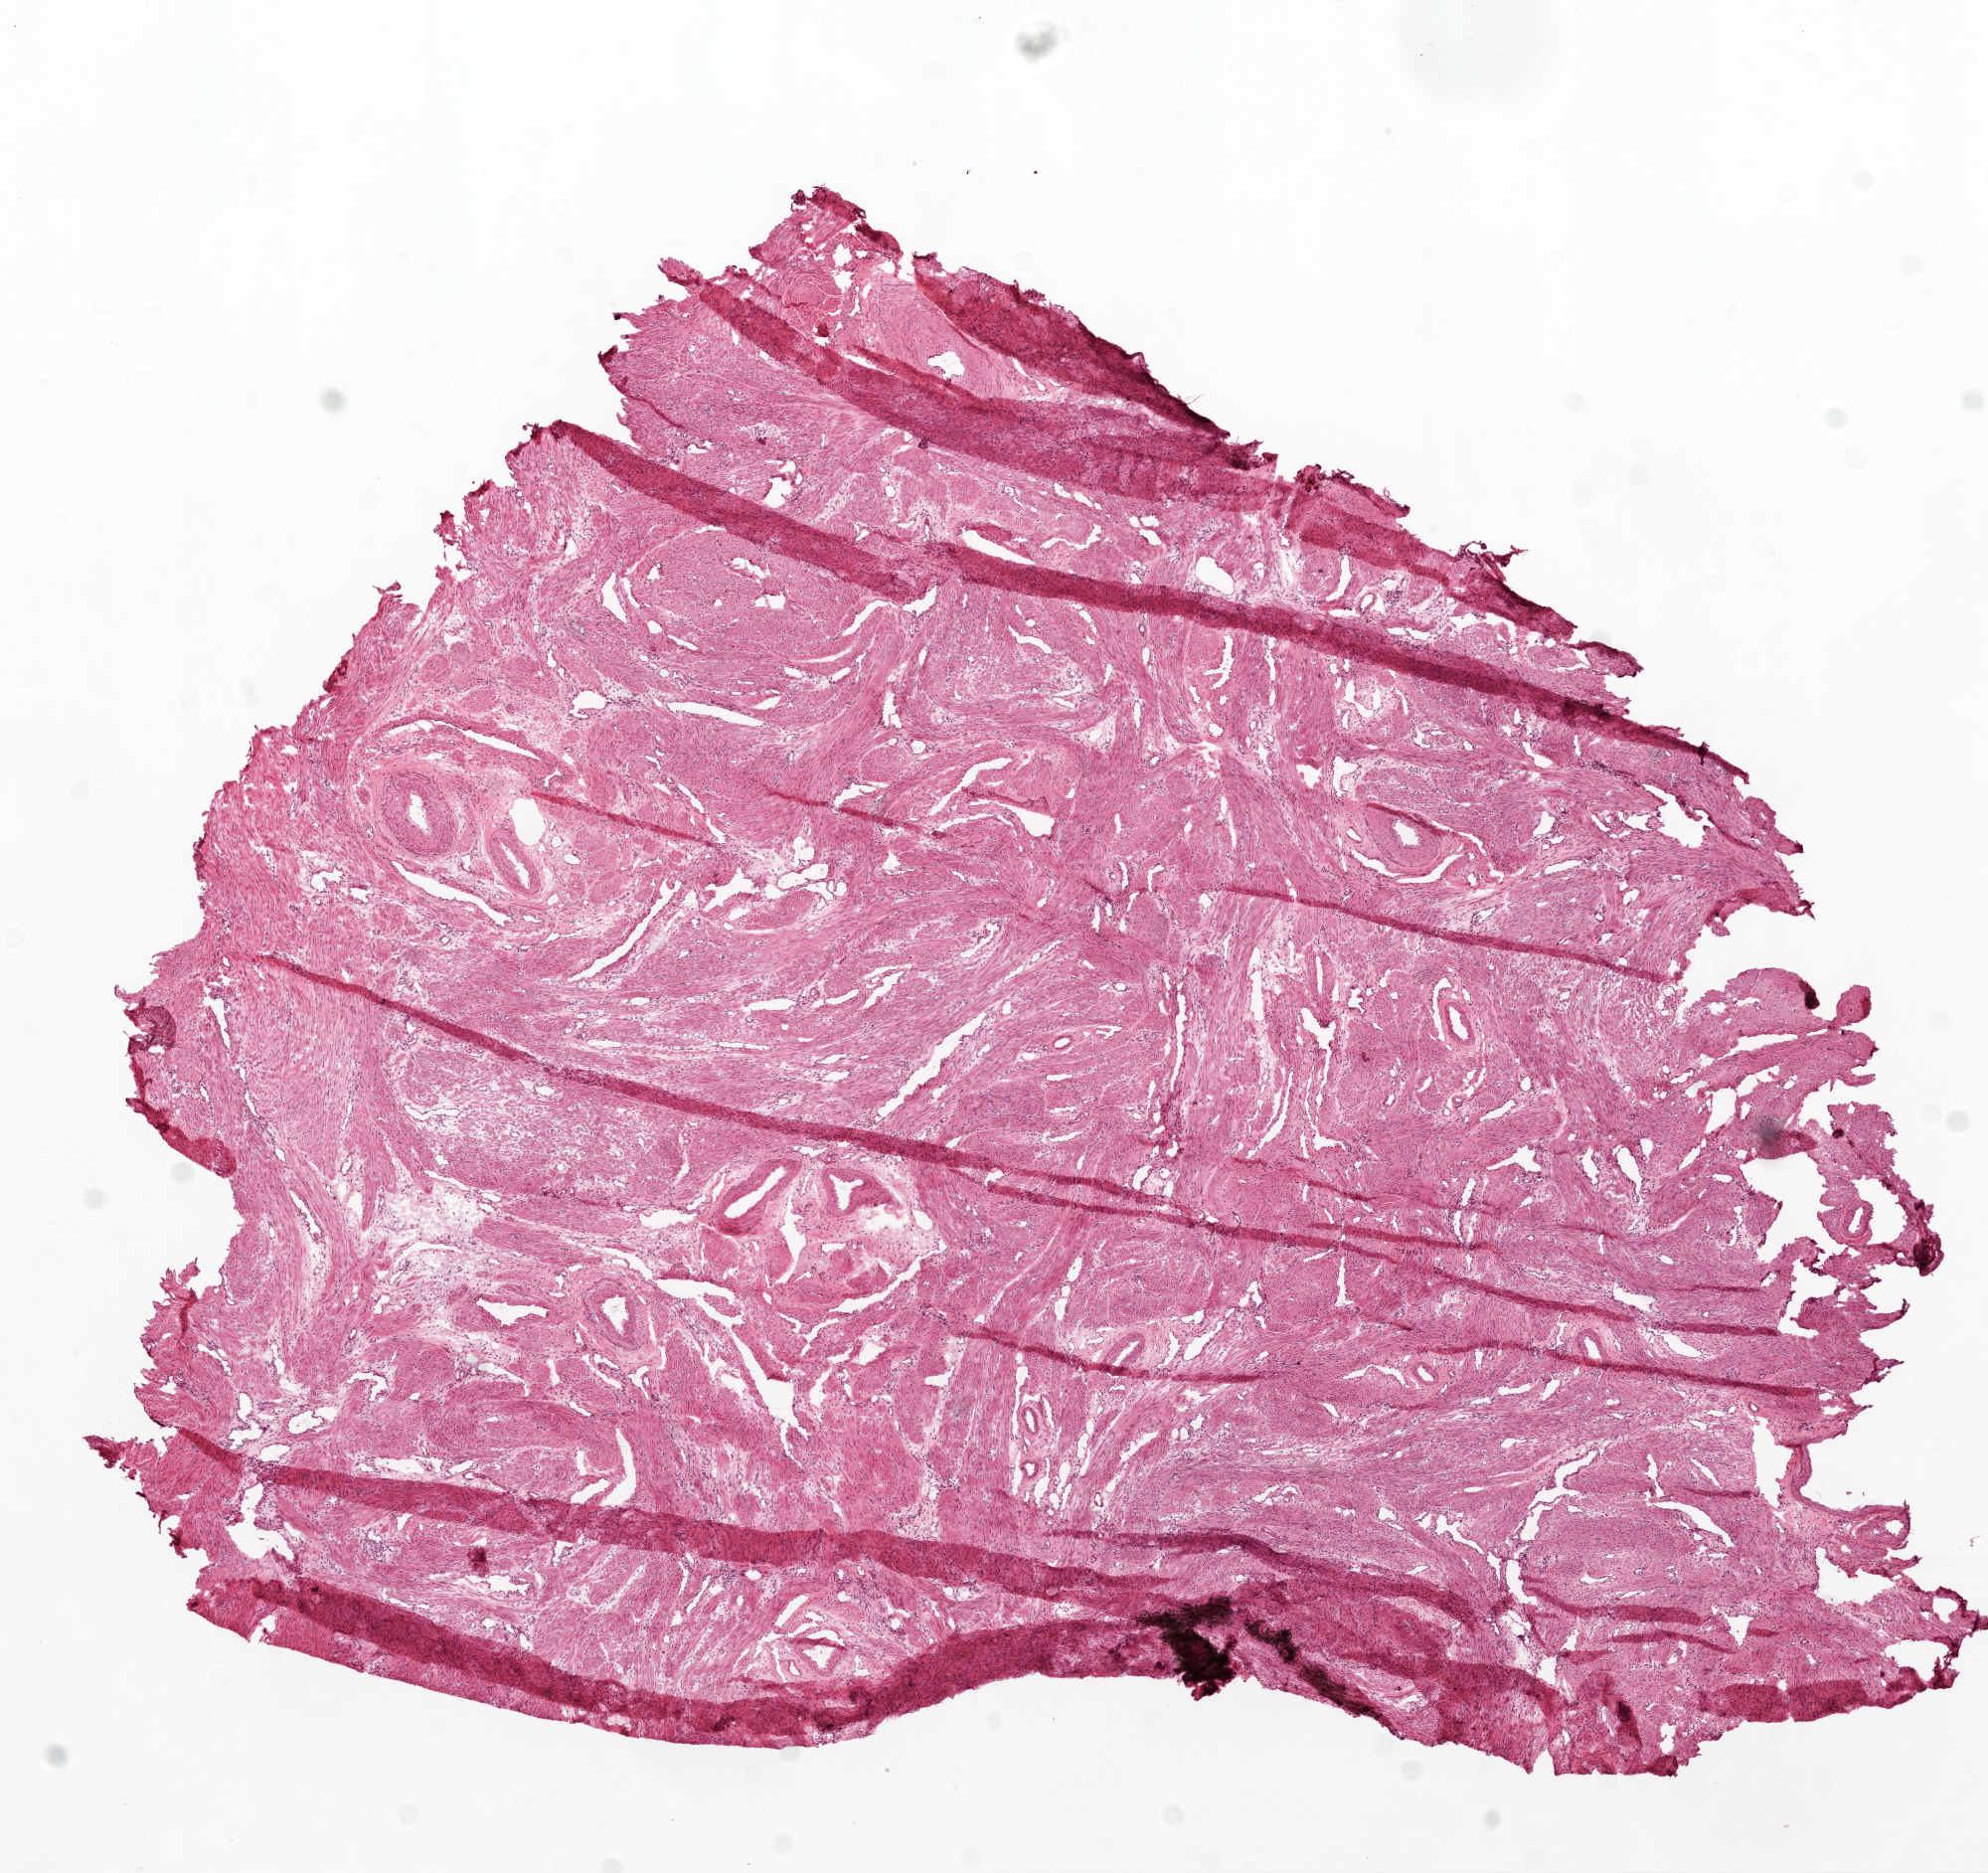
H&E whole-slide image — a low-resolution overview of the entire scanned area, about 8.0 x 7.6 mm, frozen section, ovary, solid tissue normal (non-tumour tissue) sample. Female, age 44 years at initial diagnosis.
This section: solid tissue normal (non-tumour) sample from the same patient. Patient diagnosis: Serous cystadenocarcinoma, NOS.